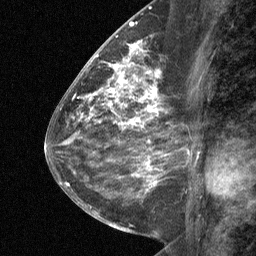
Breast MRI (dynamic contrast-enhanced), one sagittal slice; position 30 of 64 along the scan axis; dynamic contrast-enhanced study with each time point stored as its own series, time point 2 of 3 at this slice position (early post-contrast, ordered by acquisition time); 1.5 T; TE 4.8 ms, TR 27 ms; 2 mm slice thickness; 256 × 256 image matrix. Female patient, age 59 years. From the clinical record (not read from this slice): setting: breast cancer imaged before/during neoadjuvant chemotherapy; receptor status: triple-negative.
Annotated regions visible in this slice (semi-automatic segmentation, software-assisted and operator-edited):
- analysis volume of interest (the breast-tissue region the enhancement analysis was run in; not a lesion): bounding box [x1, y1, x2, y2] px = [122, 58, 164, 109]
- tumour enhancement mask (voxels above the 90 % enhancement threshold inside the analysis volume of interest): [122, 58, 160, 108]